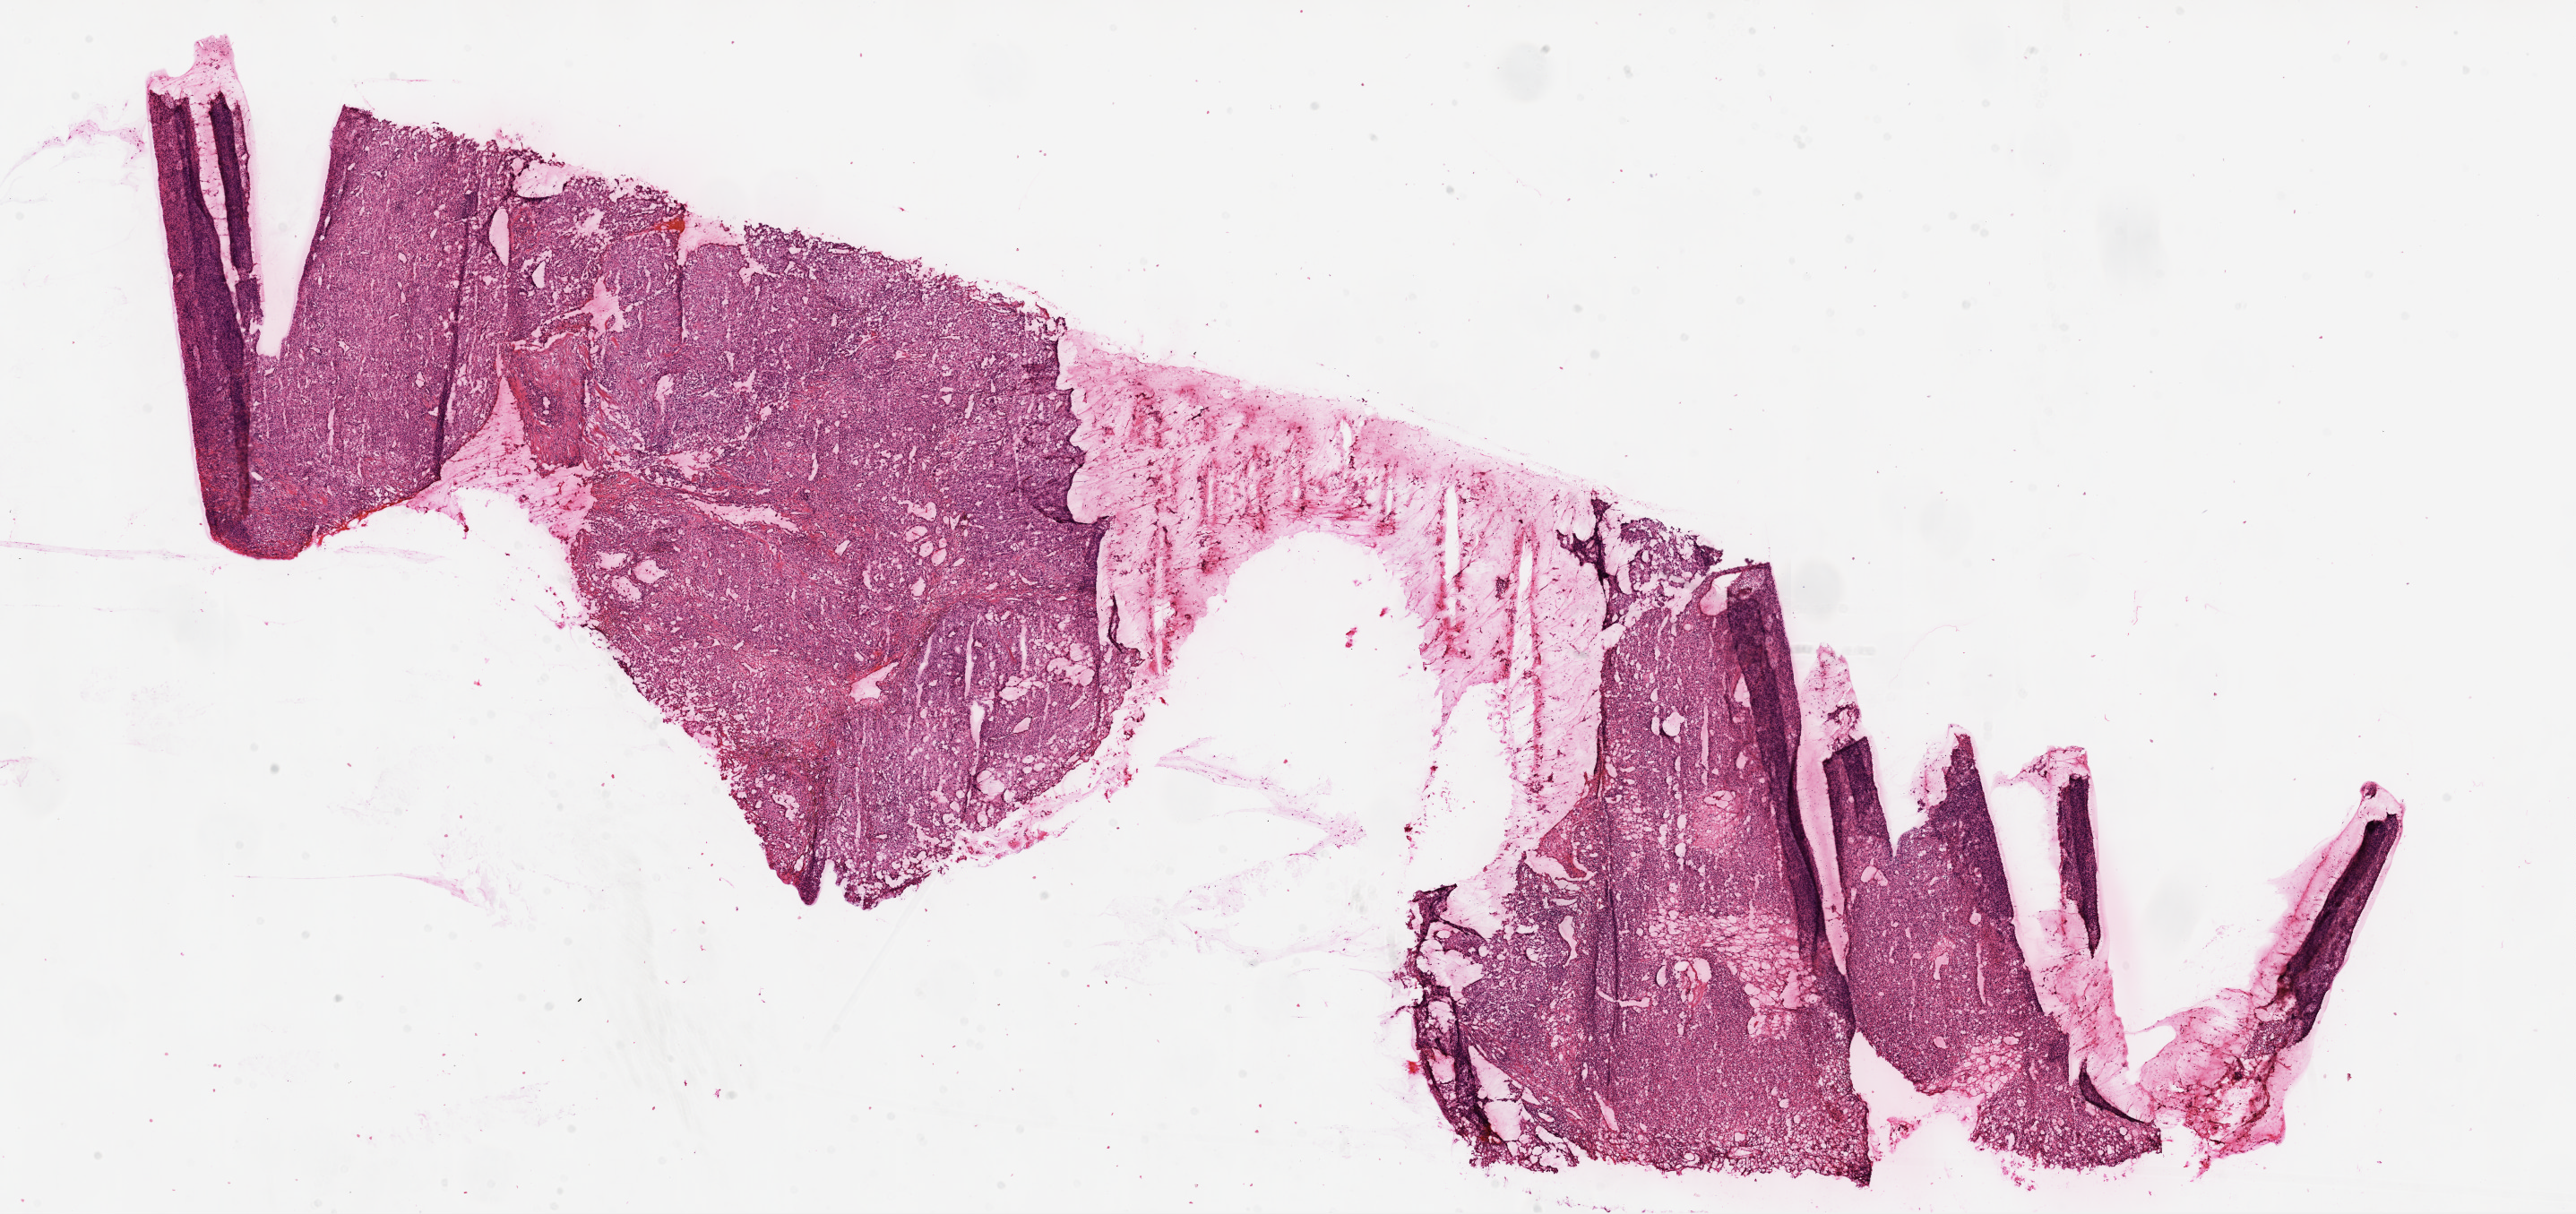
H&E-stained whole-slide image, a low-resolution overview of the entire scanned area, about 23.1 x 10.9 mm (slide scanned at 20x); frozen section from the top of the tissue portion; kidney, primary tumour sample. Patient: female, age at initial diagnosis 64 years. Histologic grade: G2 (moderately differentiated). Slide review estimates, as recorded: tumour cells 90%, tumour nuclei 85%, normal cells 0%, stromal cells 10%, necrosis 0%.
Diagnosis: Clear cell adenocarcinoma, NOS. AJCC pathologic stage: I.